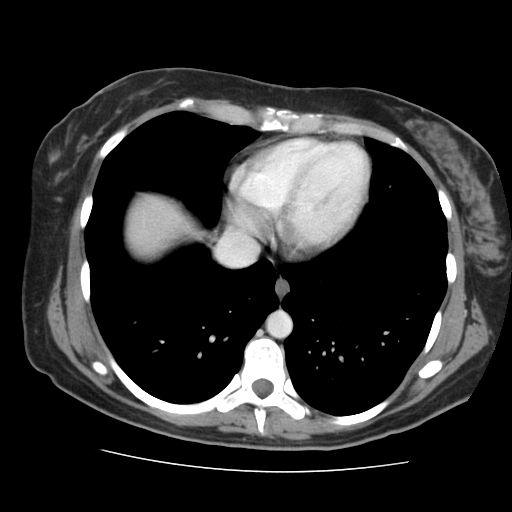
Contrast-enhanced abdominal CT, one axial slice. Position 139 of 144 along the scan axis. 120 kVp. Intravenous contrast given. Soft-tissue window (W 400 / L 40 HU). 512 × 512 image matrix, field of view 333 × 333 mm. Female patient, age 46 years. Case-level facts recorded for this patient, not image findings: diagnosis: colorectal cancer liver metastases, imaged before liver resection; multiple liver metastases: no.
Annotated regions visible in this slice (manually delineated by an expert):
- hepatic veins: bounding box (x1, y1, x2, y2) in pixels: (217, 239, 253, 266)
- liver: (128, 197, 186, 251)
- planned liver remnant (the part of the liver to remain after resection): (128, 197, 186, 251)